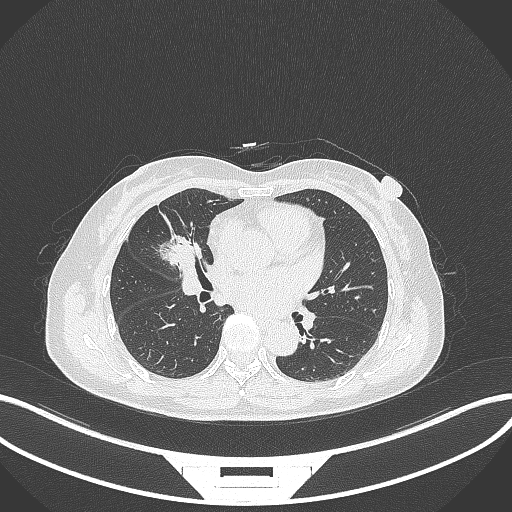
Chest CT, one axial slice; slice 152 of 284 in the series (ordered by position); reconstruction kernel B70f; 120 kVp; lung window (W 1500 / L -600 HU); 1 mm slice thickness; 512 × 512 image matrix. Female patient, age 51 years. From the clinical record (not read from this slice): clinical TNM (as recorded): T1c N0 M0.
Annotated regions visible in this slice (bounding box drawn by a radiologist):
- lung tumour (recorded histology: adenocarcinoma): bounding box (x1, y1, x2, y2) in pixels: (158, 228, 206, 275)